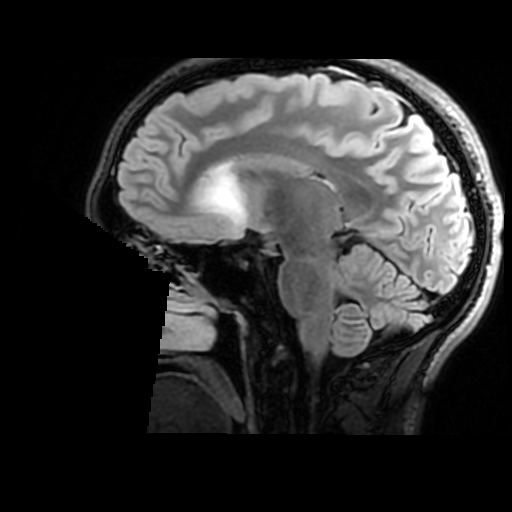
Brain MRI from a brain-tumour surgery series, one sagittal slice; position 97 of 176 along the scan axis; T2 FLAIR; 1 mm slice thickness; 512 × 512 image matrix, field of view 240 × 240 mm. Case-level facts recorded for this patient, not image findings: histopathology: Astrocytoma; WHO grade: 2; IDH mutation: yes; tumour location: Right Insular.
Outlined on this slice (expert manual segmentation):
- tumour: bounding box <195,173,246,223> (left, top, right, bottom; pixels)